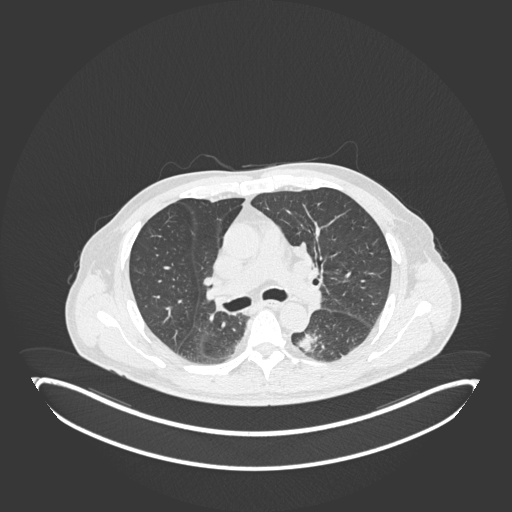
Chest CT, one axial slice; slice 130 of 251 in the series (ordered by position); reconstruction kernel B30f; lung window (W 1500 / L -600 HU); 512 × 512 image matrix. Male patient, age 72 years. Case-level facts recorded for this patient, not image findings: clinical TNM (as recorded): T2b N0 M1.
Annotated regions visible in this slice (rectangle marked by the reading radiologist):
- lung tumour (recorded histology: adenocarcinoma): box from (x=295, y=331) to (x=320, y=357) px